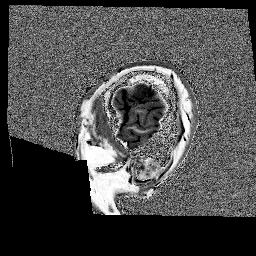
Brain MRI from a brain-tumour surgery series, one sagittal slice. Position 25 of 176 along the scan axis. 1 mm slice thickness. 256 × 256 image matrix. From the clinical record (not read from this slice): histopathology: Glioblastoma; WHO grade: 4; IDH mutation: no.
Annotated regions visible in this slice (manually delineated by an expert):
- tumour: bounding box (x1, y1, x2, y2) in pixels: (133, 85, 155, 97)